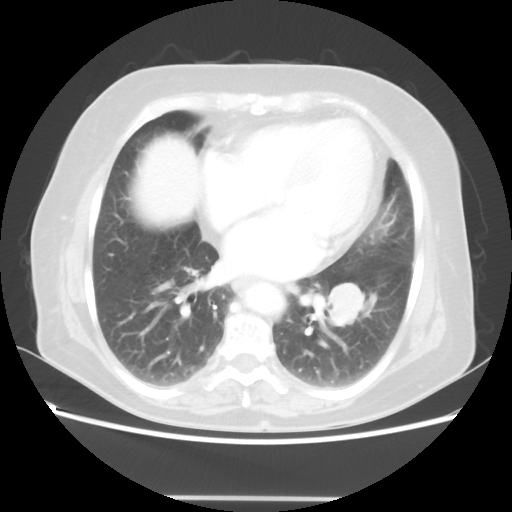
Chest CT, one axial slice. Slice 24 of 56 in the series (ordered by position). Reconstruction kernel STANDARD. 100 kVp. Lung window (W 1500 / L -600 HU). 5 mm slice thickness. 512 × 512 image matrix, field of view 360 × 360 mm. Patient: female, 73 years. From the clinical record (not read from this slice): clinical TNM (as recorded): T1c N0 M0.
Outlined on this slice (bounding box drawn by a radiologist):
- lung tumour (recorded histology: adenocarcinoma): box from (x=323, y=280) to (x=370, y=330) px